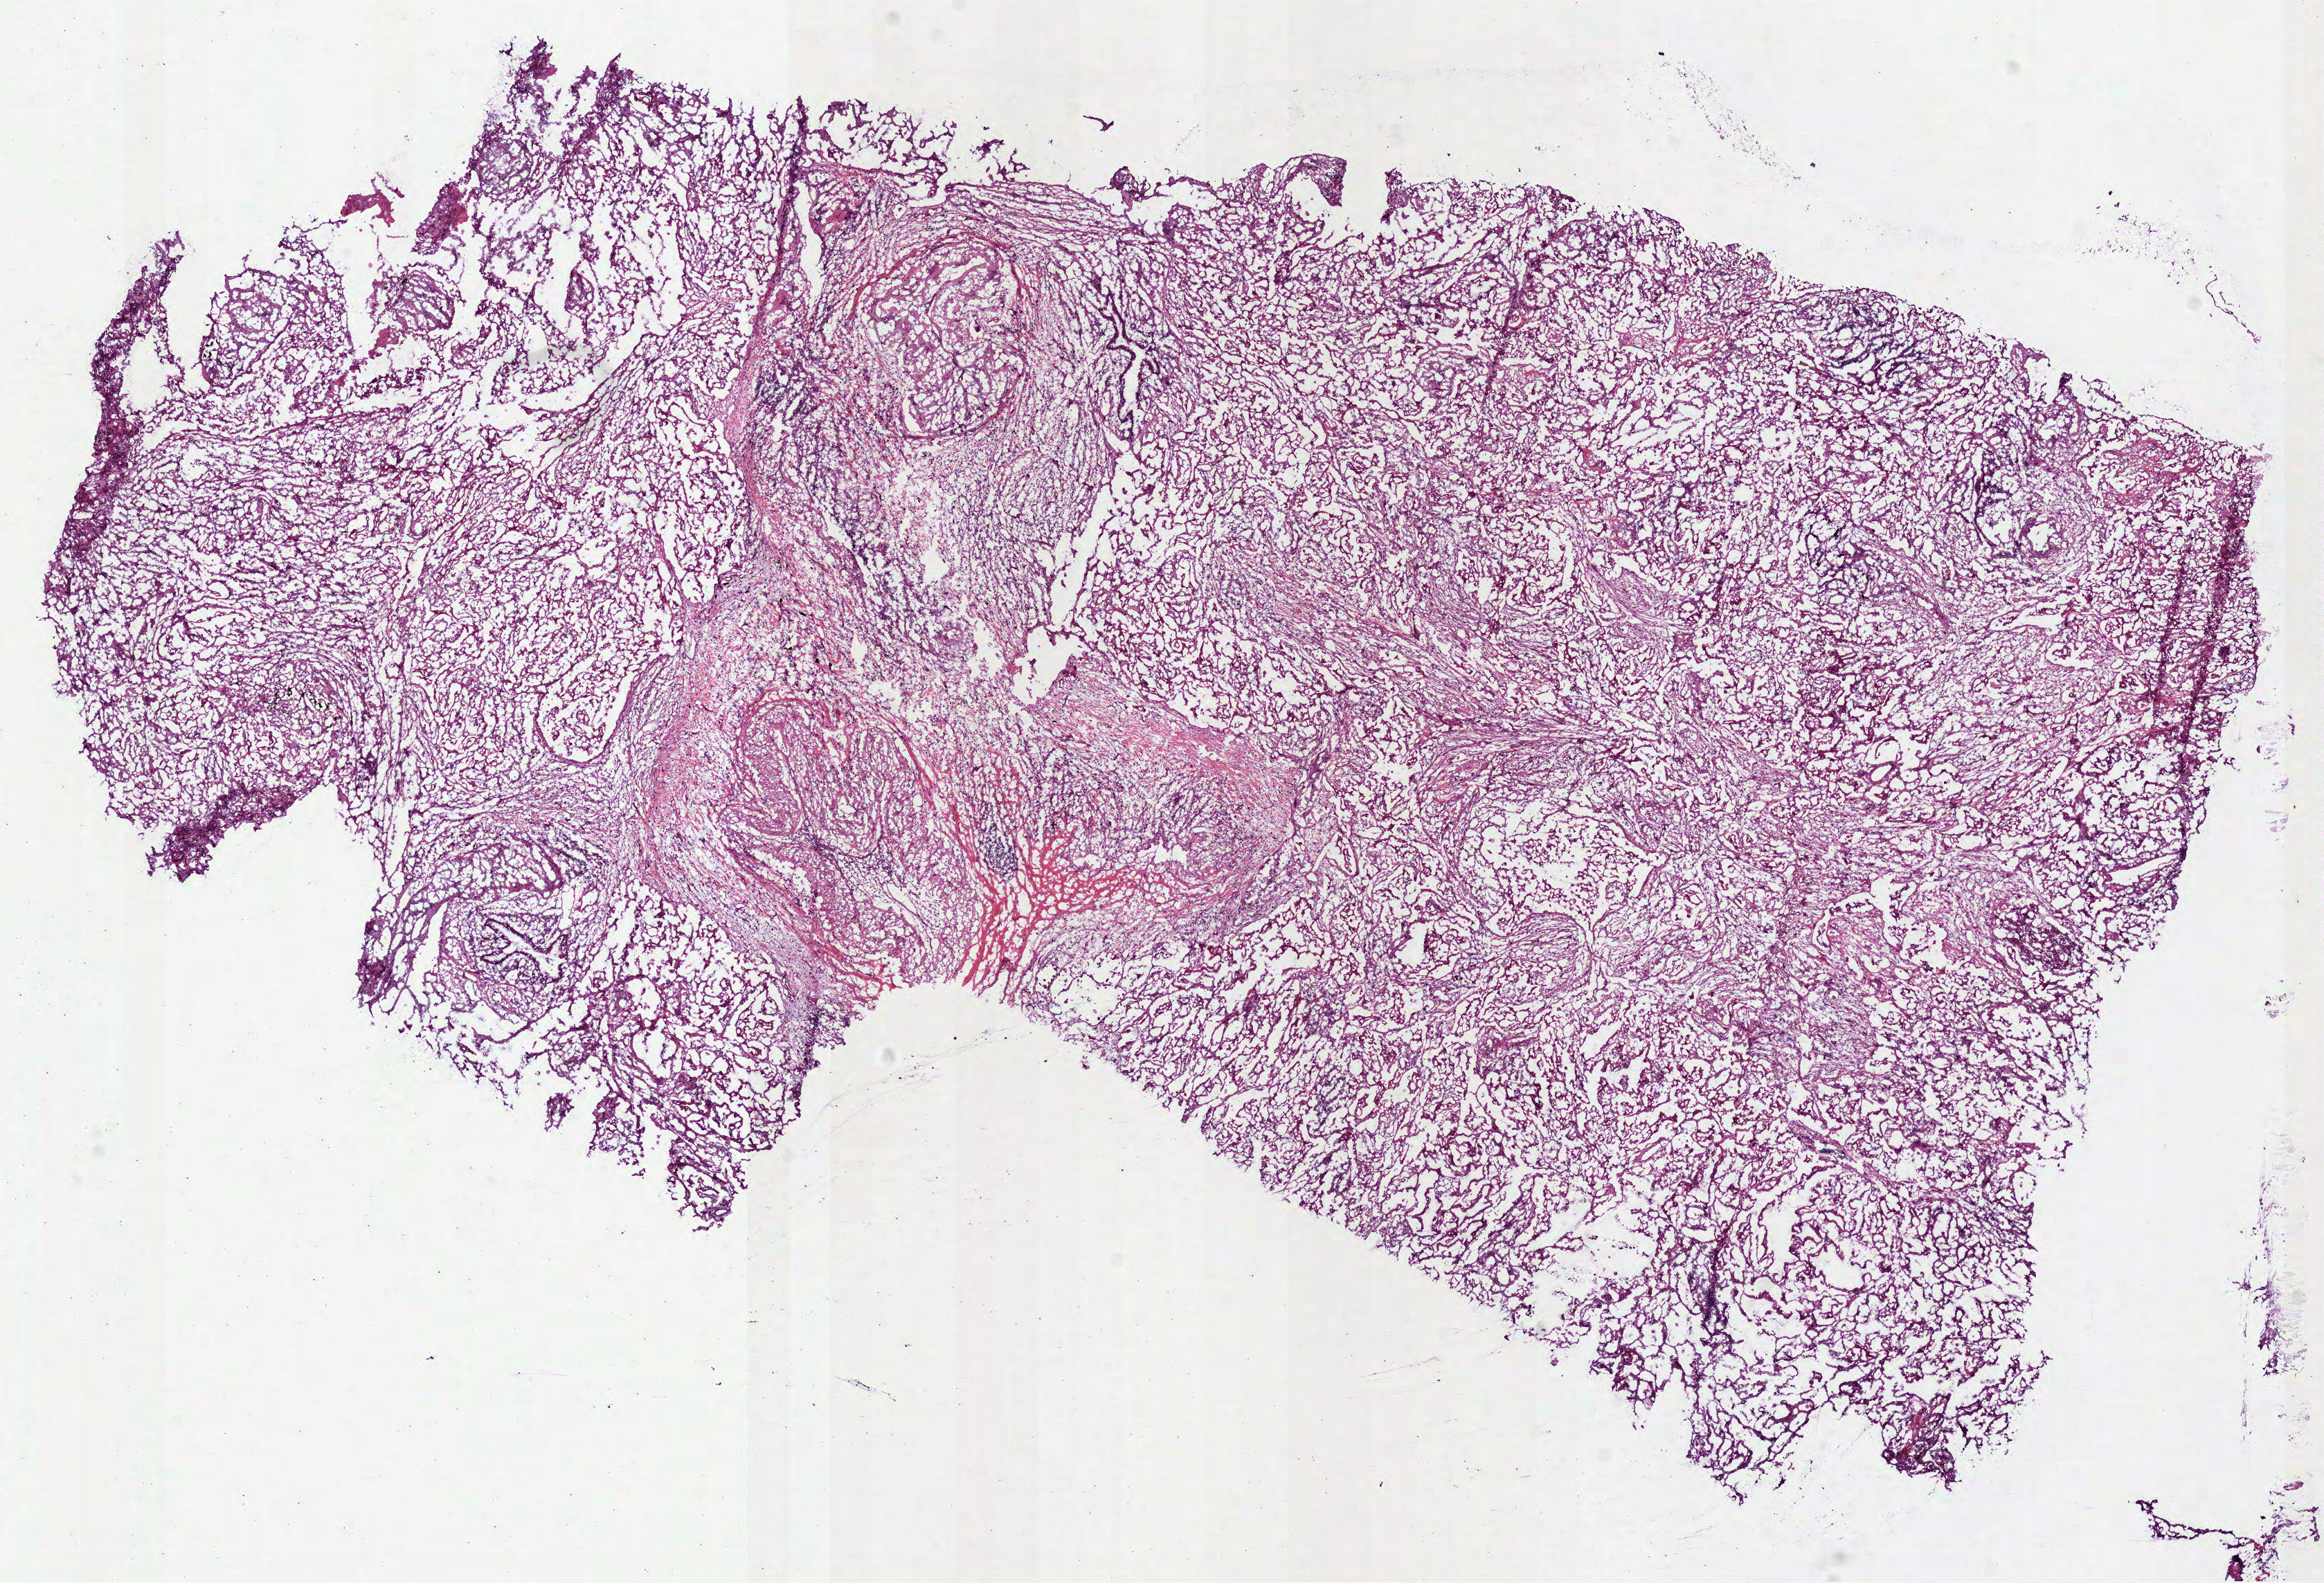
Digitized H&E-stained tissue section (whole slide), low-resolution overview of the scanned area, about 13.5 x 9.2 mm, frozen section, primary tumour sample from the lung. Patient: male, age at initial diagnosis 68 years. Composition of this section per pathologist review: tumour cells 75%, tumour nuclei 65%, normal cells 15%, stromal cells 10%, necrosis 0%. Infiltration values recorded for this section: lymphocyte infiltration 15%, monocyte infiltration 5%.
- laterality: right
- histologic diagnosis: Mucinous adenocarcinoma (lower lobe, lung)
- AJCC pathologic stage: IIB (7th edition)
- TNM: T3 N0 M0